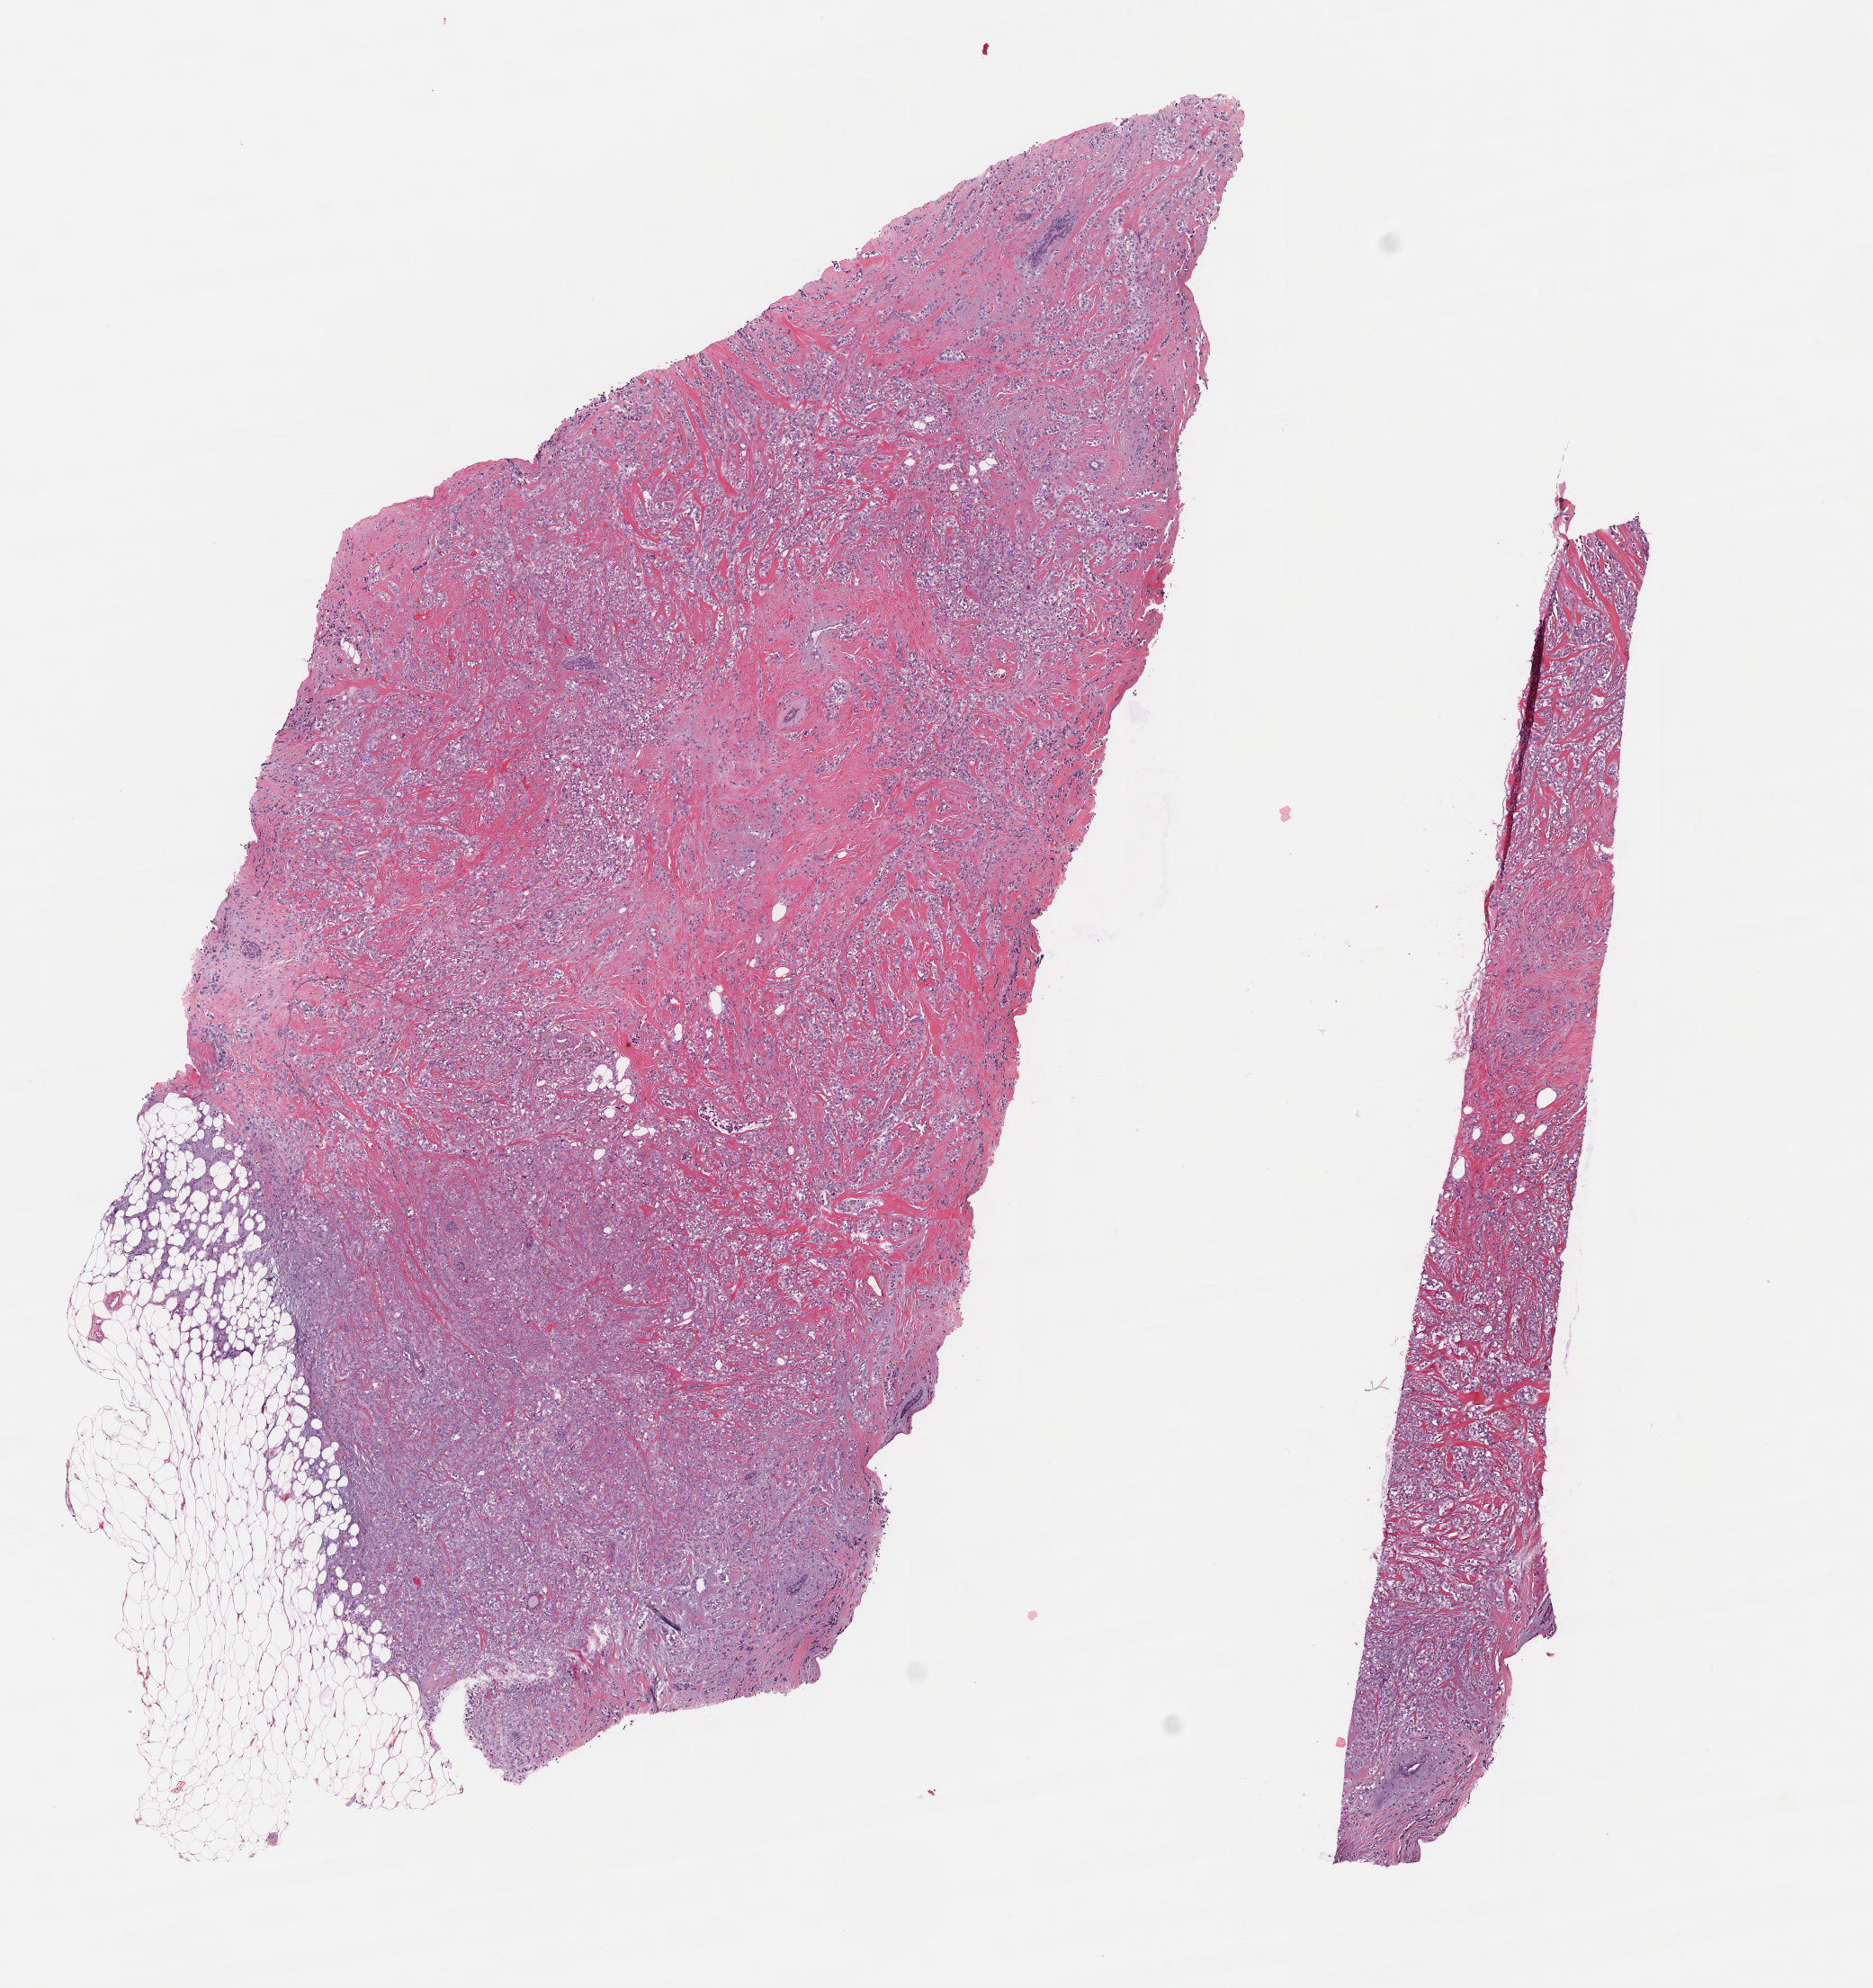
H&E-stained whole-slide image — low-resolution overview of the scanned area, about 8.2 x 8.7 mm; frozen section from the bottom of the tissue portion; primary tumour sample from the breast. Female, age 71 years at initial diagnosis. Slide review estimates, as recorded: tumour cells 79%, tumour nuclei 80%, normal cells 1%, stromal cells 20%, necrosis 0%. Inflammatory infiltration, as recorded: lymphocyte infiltration 2%, monocyte infiltration 0%, neutrophil infiltration 0%.
Diagnosis: Lobular carcinoma, NOS. AJCC pathologic stage: IIIA. TNM: T3 N1a MX.